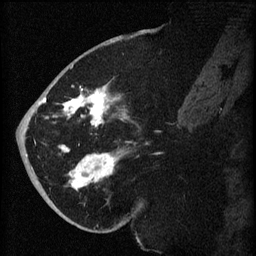
Breast MRI (dynamic contrast-enhanced), one sagittal slice; slice 31 of 60 in the series (ordered by position); dynamic contrast-enhanced series, image 2 of 3 at this slice position (ordered by acquisition); 1.5 T; TE 4.2 ms, TR 8.2 ms; 2 mm slice thickness; 256 × 256 image matrix, field of view 180 × 180 mm. Patient: female, 71 years.
Annotated regions visible in this slice (semi-automatic segmentation, software-assisted and operator-edited):
- analysis volume of interest (the breast-tissue region the enhancement analysis was run in; not a lesion): bounding box [x1, y1, x2, y2] px = [40, 72, 141, 196]
- tumour enhancement mask (voxels above the 70 % enhancement threshold inside the analysis volume of interest): [40, 85, 122, 189]